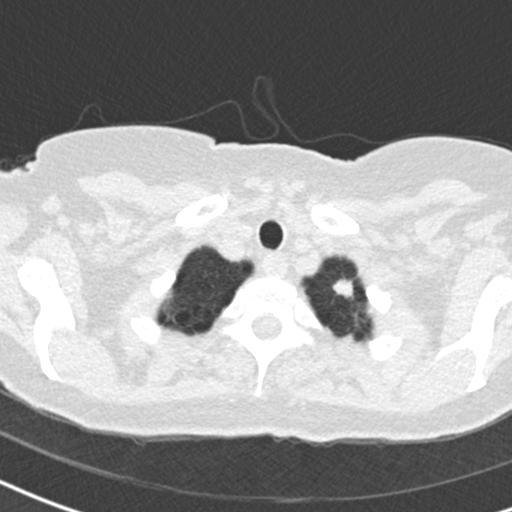
Low-dose screening chest CT, one axial slice. Slice 173 of 184 in the series (ordered by position). Reconstruction kernel B30f. 120 kVp. Lung window (W 1500 / L -600 HU). 2 mm slice thickness. 512 × 512 image matrix, field of view 280 × 280 mm.
Structures marked on this image (outlined manually by an expert reader):
- lesion 1 (tumor, upper lobe of left lung): bounding box [x1, y1, x2, y2] px = [333, 279, 353, 298]